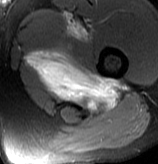
MRI of an extremity soft-tissue mass, one axial slice. Position 66 of 70 along the scan axis. T2-weighted fat-saturated. MR volume resampled by the dataset authors to the PET/CT grid (not the native acquisition matrix). 3.27 mm slice thickness. 158 × 164 image matrix. Male patient. Case-level facts recorded for this patient, not image findings: histological type: extraskeletal osteosarcoma; grade: high; site of the primary tumour: left adductur.
Outlined on this slice (expert contour drawn on MRI and transferred to this co-registered scan by the dataset authors):
- gross tumour volume (mass): box from (x=24, y=12) to (x=128, y=113) px